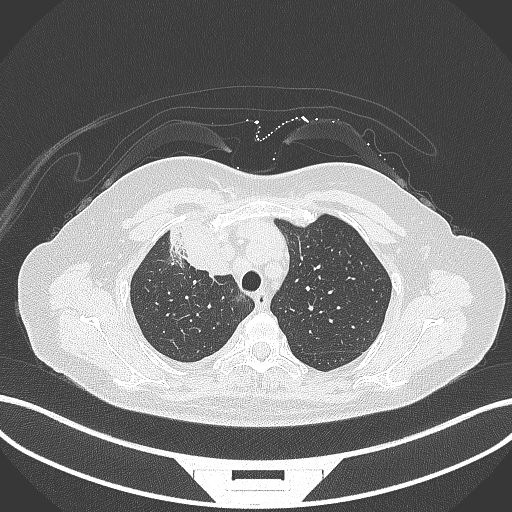
Chest CT, one axial slice; position 238 of 305 along the scan axis; reconstruction kernel B70f; 120 kVp; lung window (W 1500 / L -600 HU); 1 mm slice thickness; 512 × 512 image matrix, field of view 400 × 400 mm. Patient: female, 52 years. Case-level facts recorded for this patient, not image findings: clinical TNM (as recorded): T3 N1 M1.
Structures marked on this image (rectangle marked by the reading radiologist):
- lung tumour (recorded histology: adenocarcinoma): bounding box (x1, y1, x2, y2) in pixels: (164, 219, 233, 282)